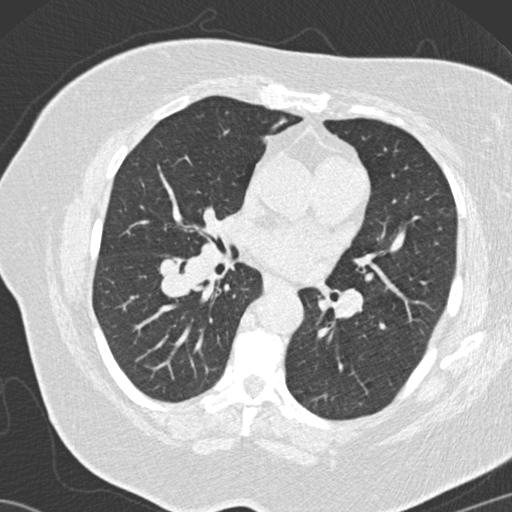
Low-dose screening chest CT, one axial slice; slice 72 of 146 in the series (ordered by position); reconstruction kernel B30f; 120 kVp; lung window (W 1500 / L -600 HU); 512 × 512 image matrix, field of view 350 × 350 mm.
Outlined on this slice (expert manual segmentation):
- lesion 4 (tumor, lower lobe of right lung): bounding box (x1, y1, x2, y2) in pixels: (160, 259, 194, 298)